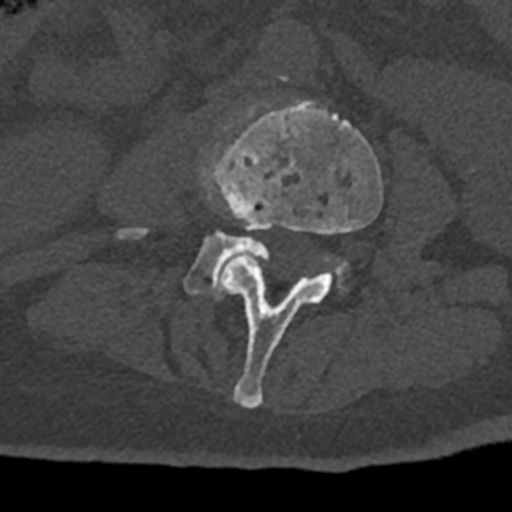
CT including the spine, one axial slice. Position 298 of 797 along the scan axis. Reconstruction kernel Br40s/3. 120 kVp. Bone window (W 1800 / L 400 HU). 0.5 mm slice thickness. 512 × 512 image matrix, field of view 160 × 160 mm. Patient: male, 74 years. From the clinical record (not read from this slice): primary cancer: renal; vertebrae with lytic lesions (as recorded): T10, L1, L2, L3, L4, L5.
Structures marked on this image (semi-automatically segmented with operator editing):
- L3 vertebra: bounding box [x1, y1, x2, y2] px = [214, 100, 383, 408]
- L4 vertebra: [117, 166, 348, 300]